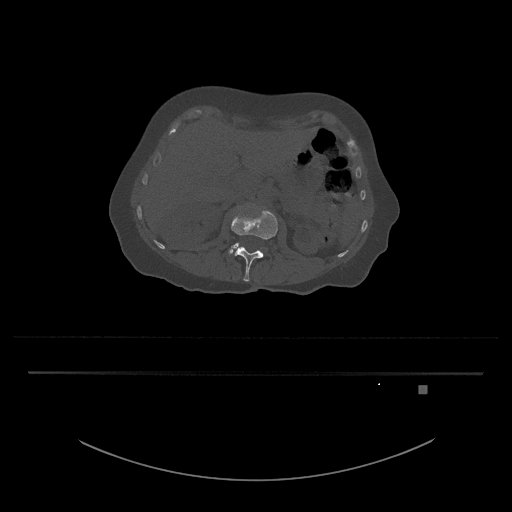
CT including the spine, one axial slice. Slice 478 of 797 in the series (ordered by position). Reconstruction kernel Br40s/3. 120 kVp. Bone window (W 1800 / L 400 HU). 512 × 512 image matrix, field of view 500 × 500 mm. Patient: female, 57 years. From the clinical record (not read from this slice): primary cancer: cervical.
Structures marked on this image (semi-automatically segmented with operator editing):
- L3 vertebra: bounding box (x1, y1, x2, y2) in pixels: (228, 242, 241, 255)